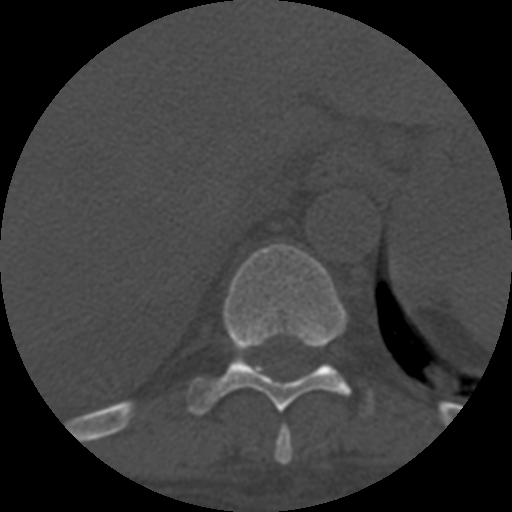
CT including the spine, one axial slice; position 357 of 708 along the scan axis; 120 kVp; one of 3 acquisitions stored at this slice position; bone window (W 1800 / L 400 HU); 1.25 mm slice thickness; 512 × 512 image matrix, field of view 160 × 160 mm. Patient age 55 years. From the clinical record (not read from this slice): primary cancer: colon; vertebrae with lytic lesions (as recorded): T12, L1, L5.
Annotated regions visible in this slice (semi-automatically segmented with operator editing):
- T10 vertebra: bounding box [x1, y1, x2, y2] px = [188, 244, 371, 415]
- T9 vertebra: [275, 426, 293, 465]